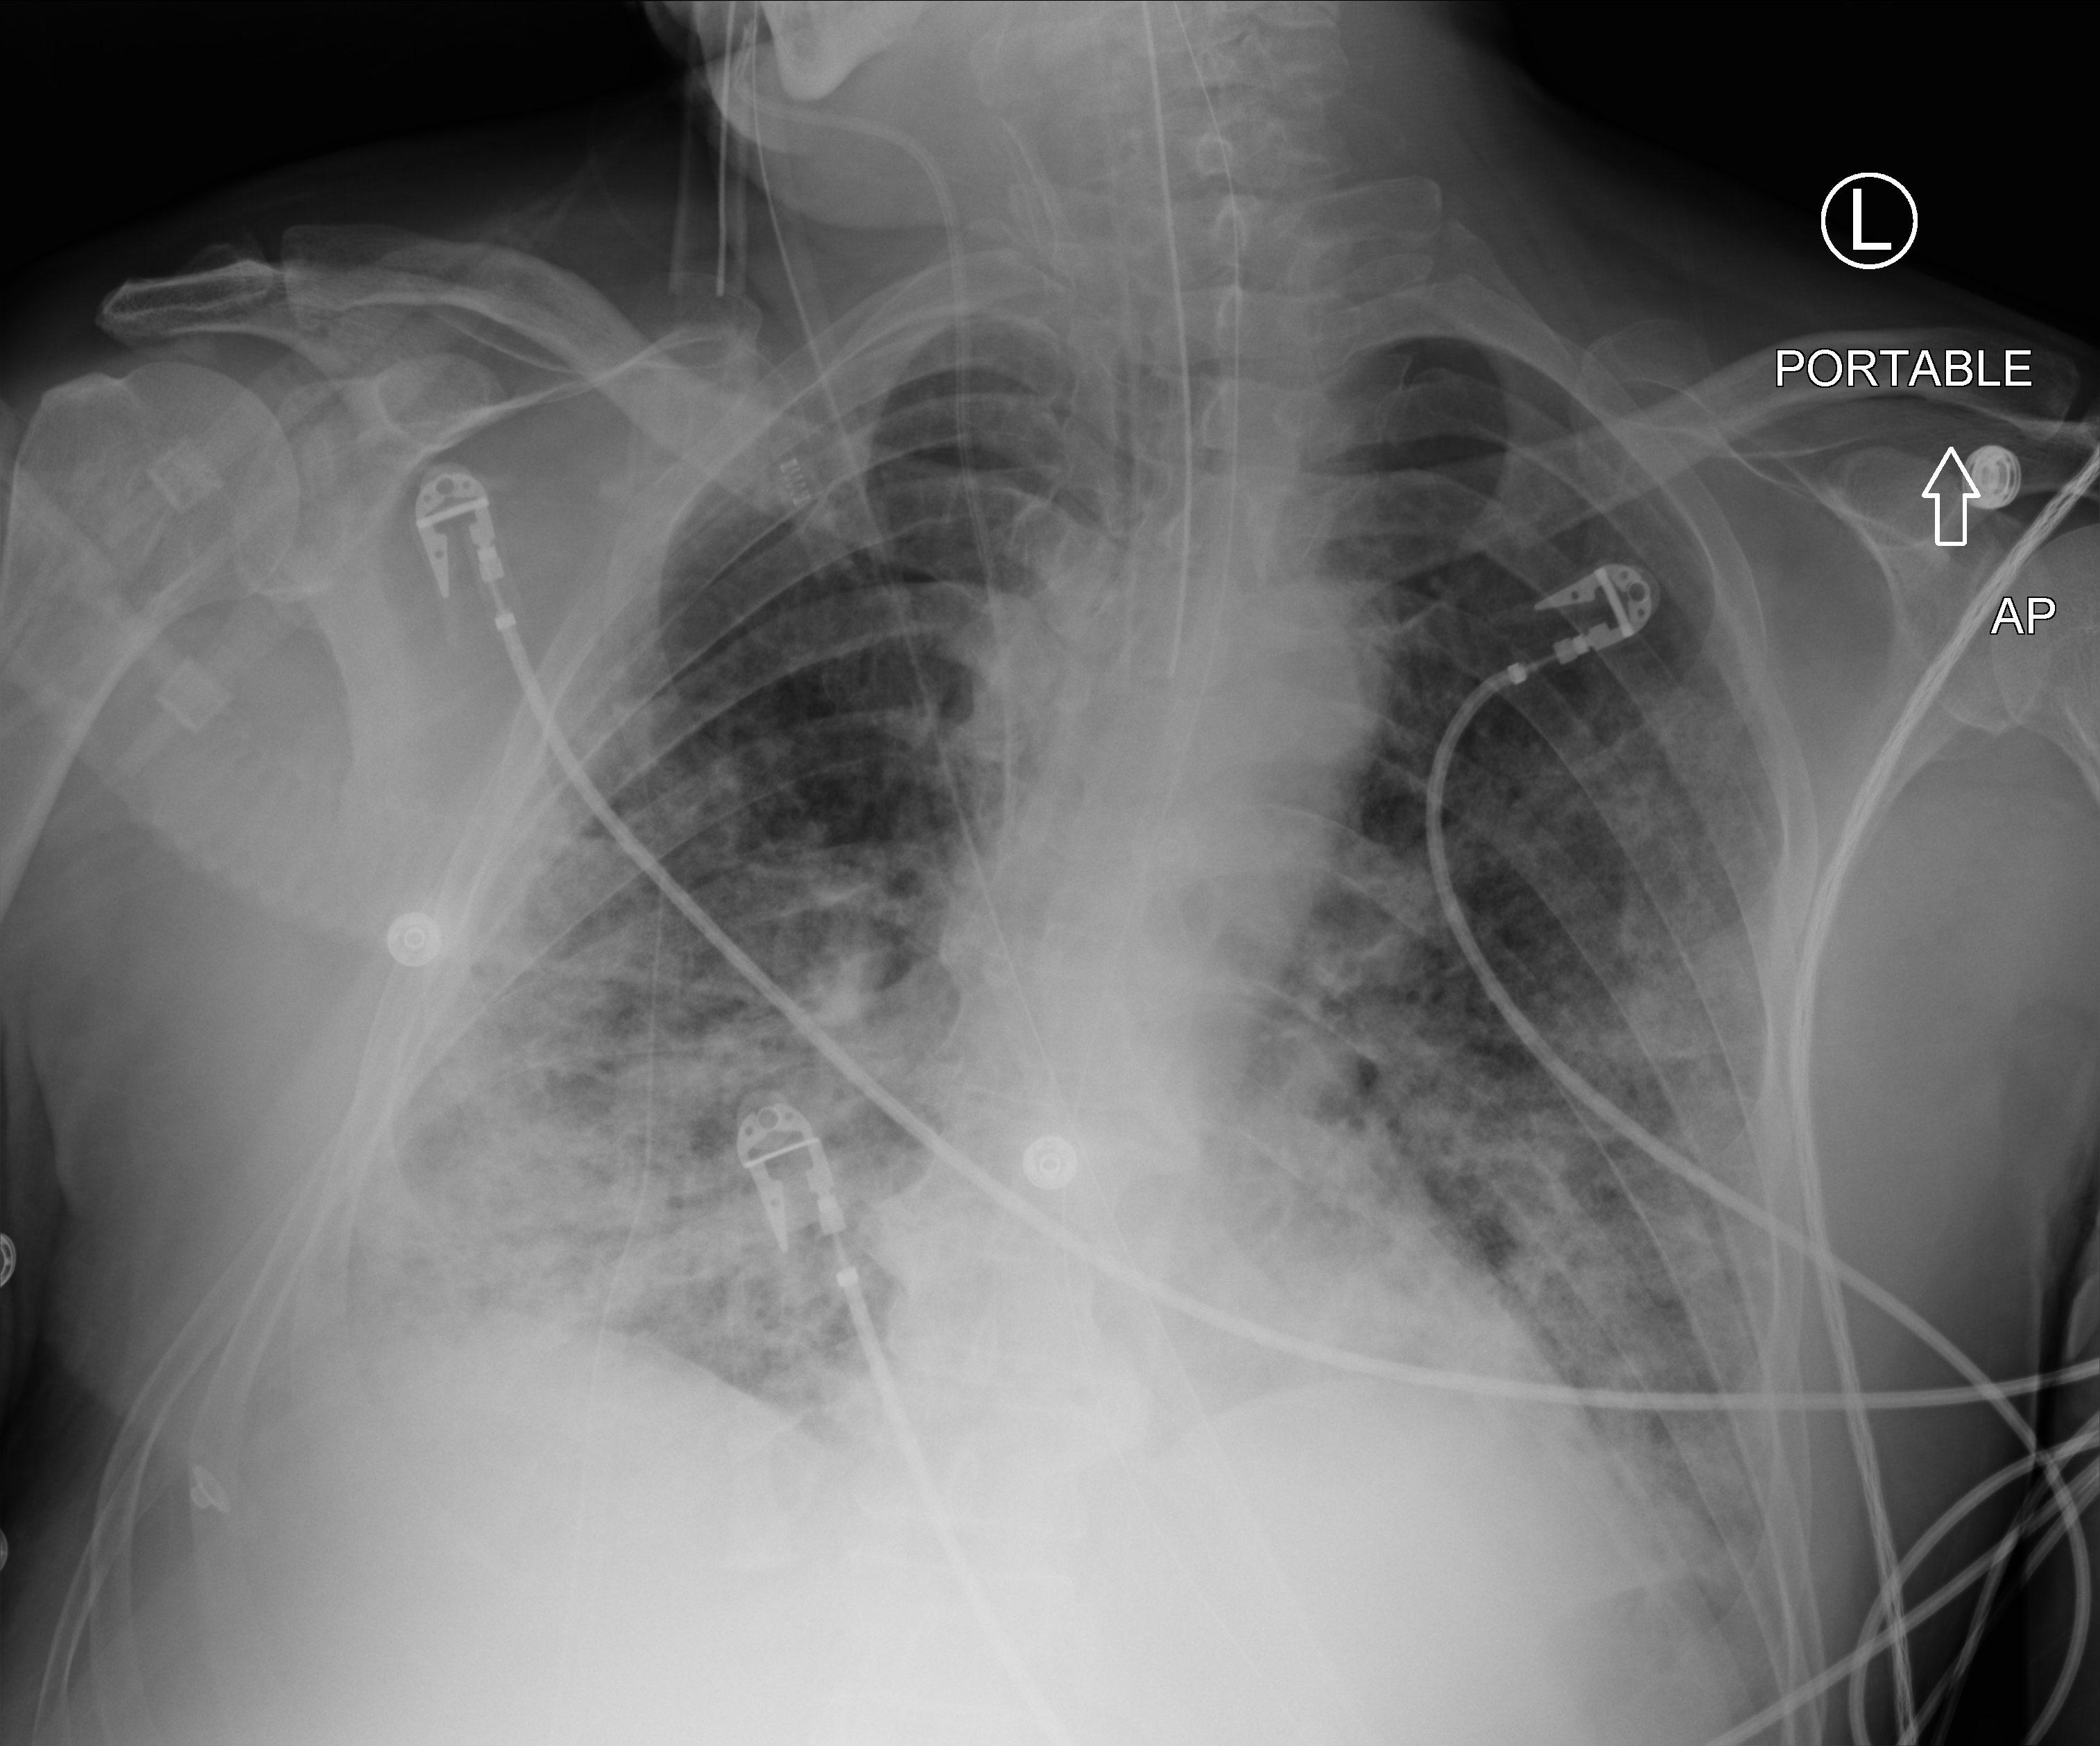
Portable chest radiograph, anteroposterior (AP) projection. Male patient hospitalised with COVID-19, age 60–74 years.
From the hospital-stay record, not from the radiograph (when in the stay this image was taken is not recorded):
- length of hospital stay: 32 days
- diabetes (admission record): yes